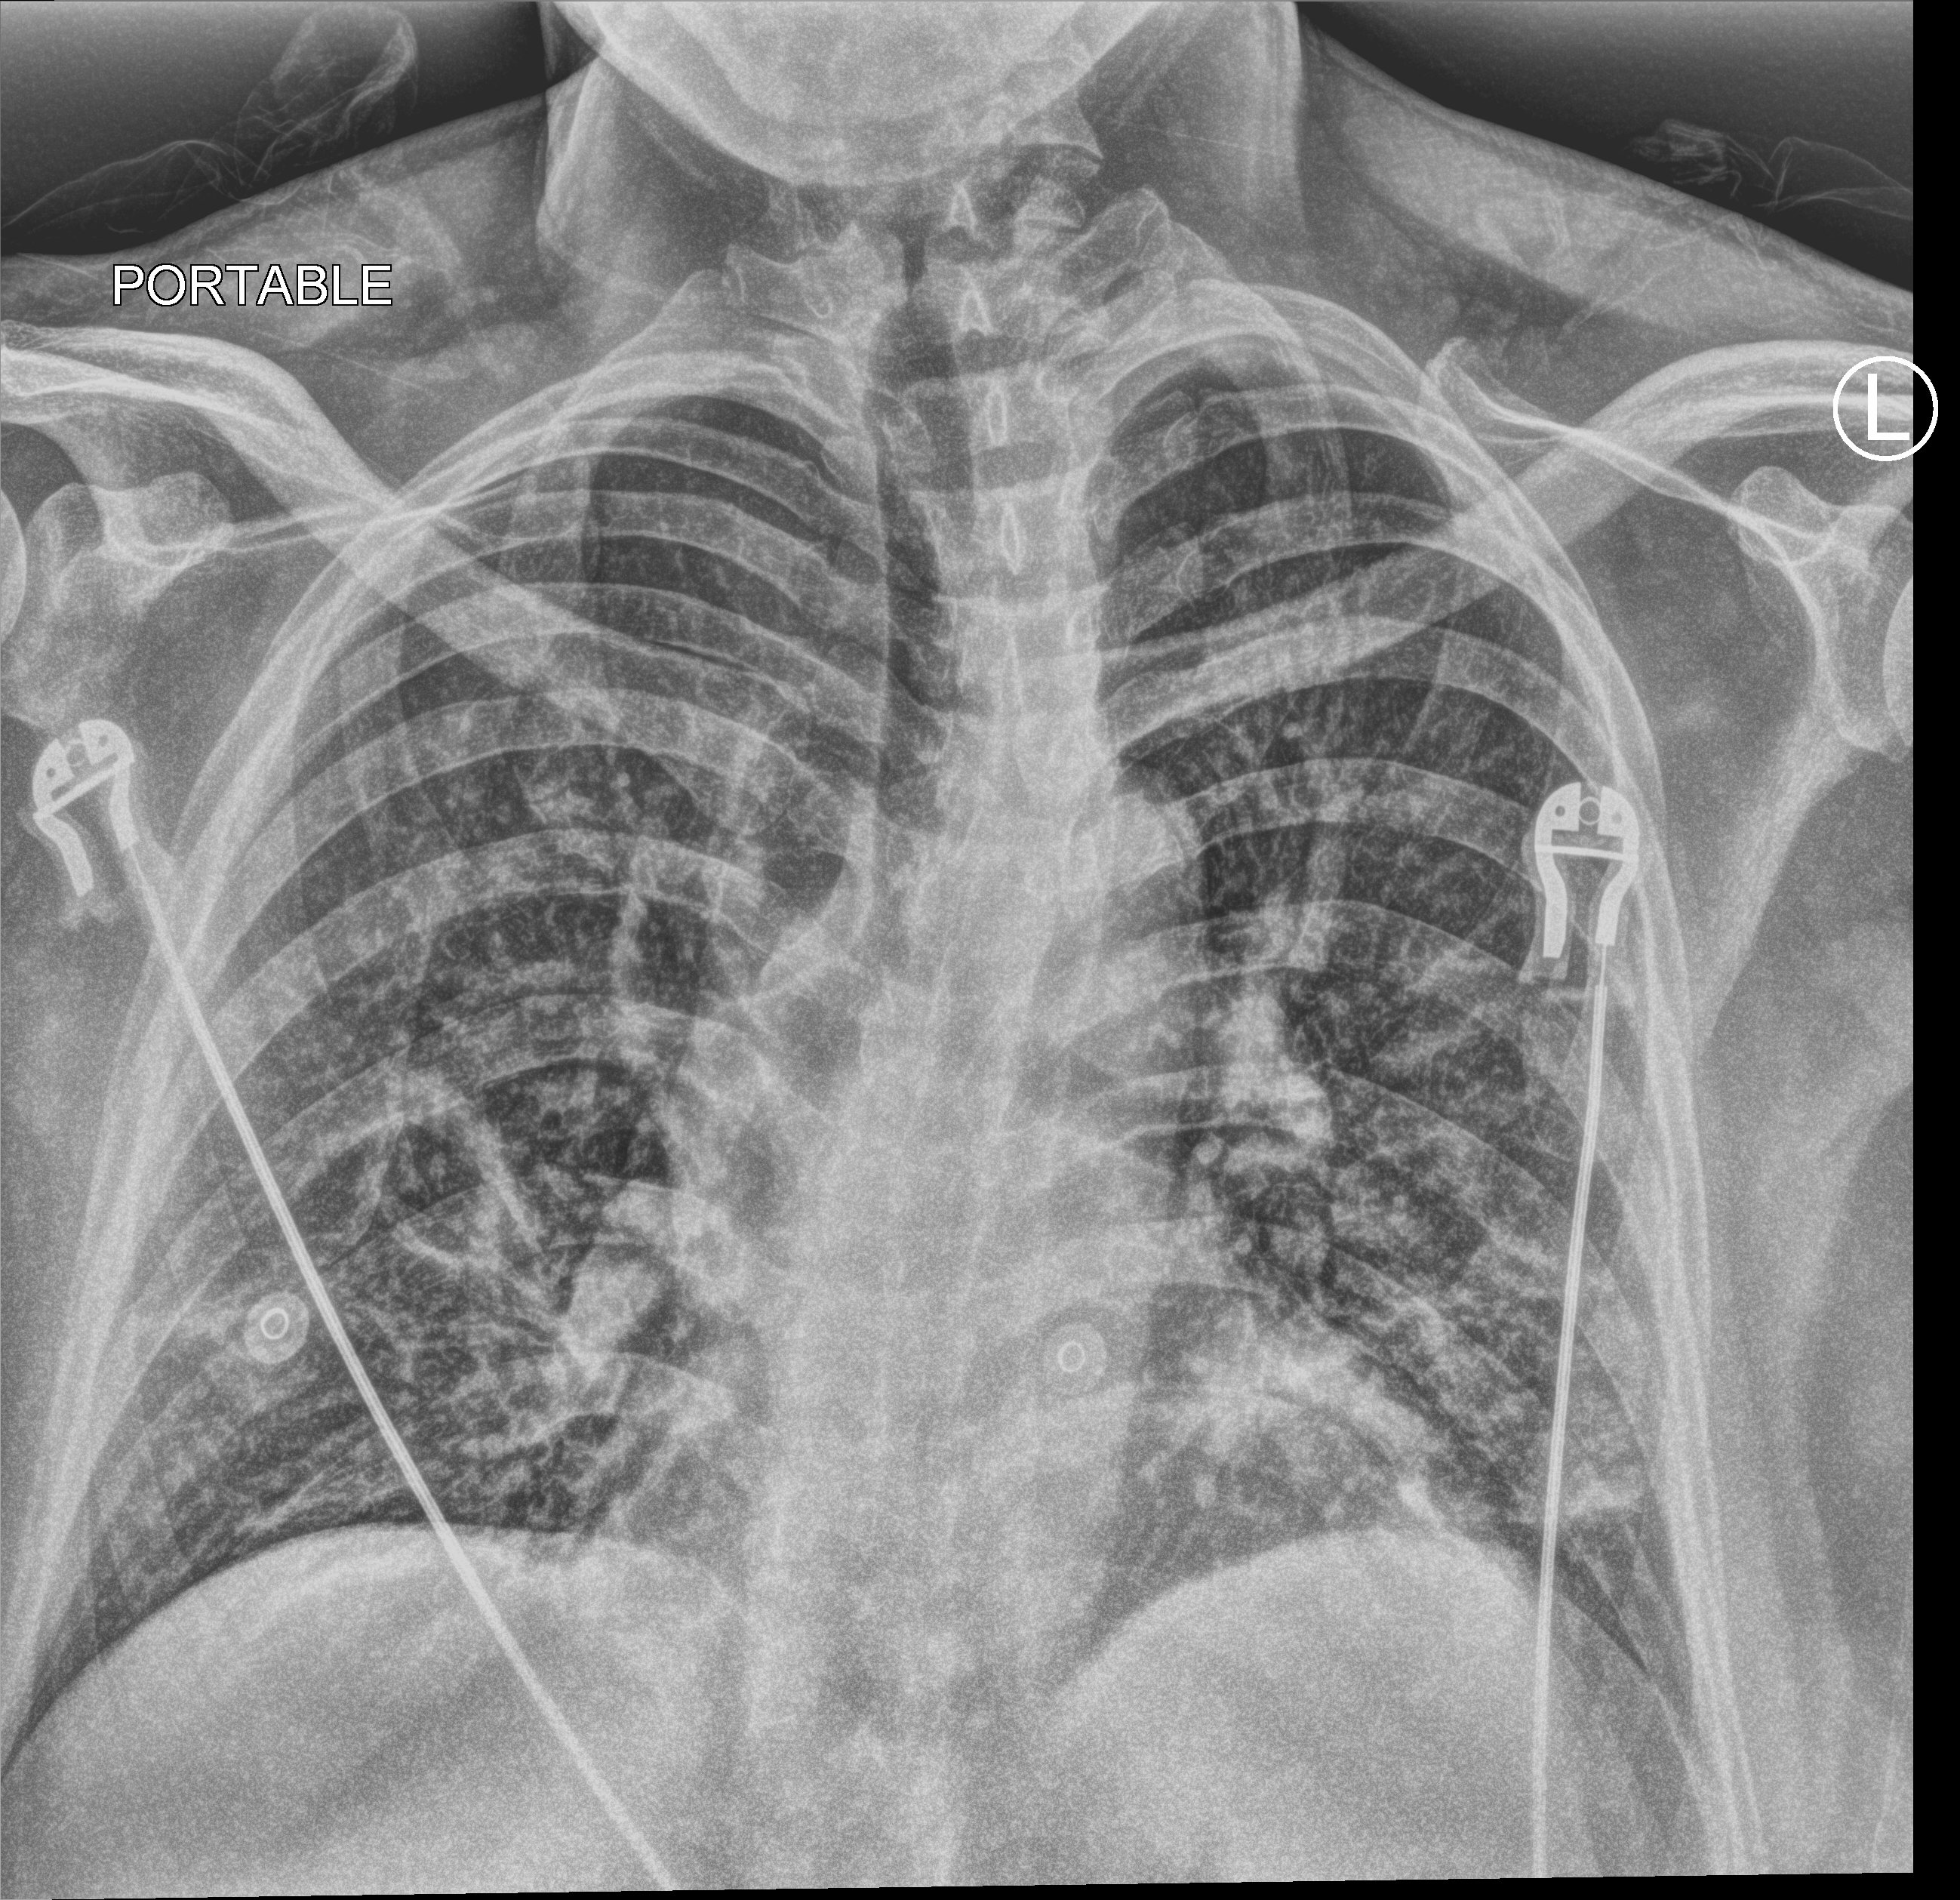
Chest X-ray (portable); anteroposterior (AP) projection. Male patient hospitalised with COVID-19, age 18–59 years.
Hospital-stay facts (about this admission, not read from this image; timing relative to this image not recorded): length of hospital stay: 2 days.